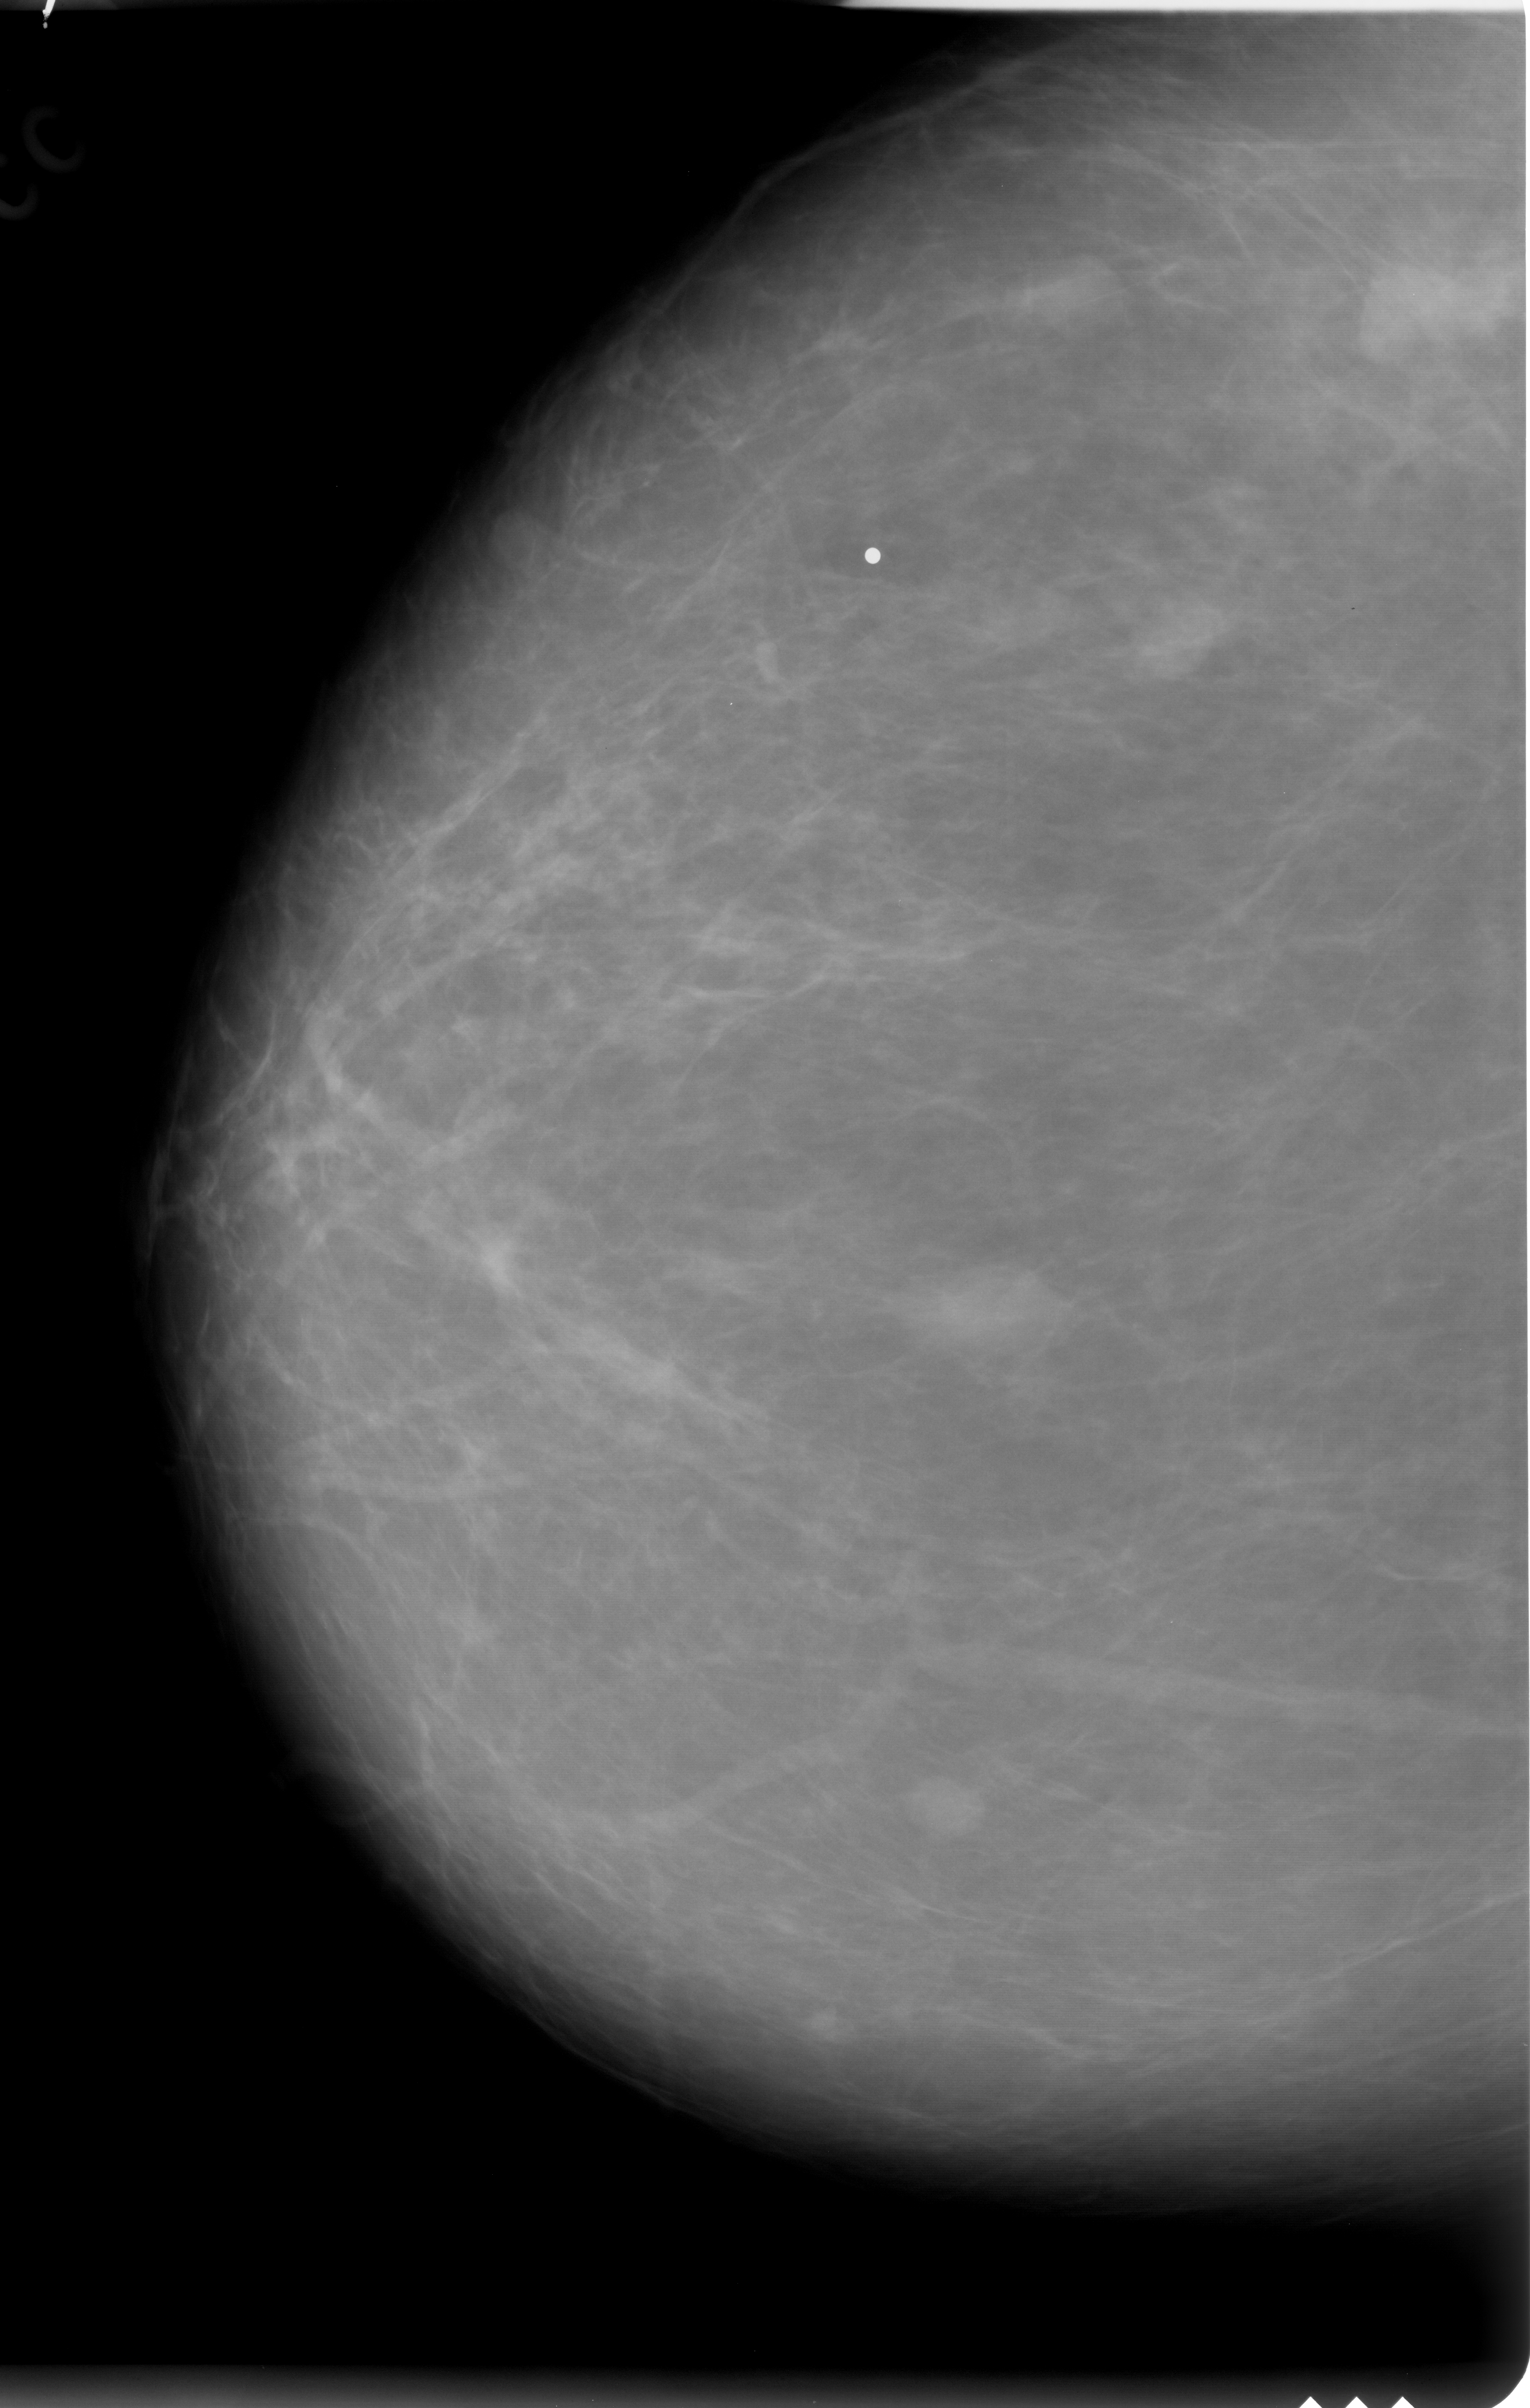
Scanned film-screen mammogram, right breast, CC view, breast composition: almost entirely fatty (BI-RADS density category 1 of 4).
- Marked findings (only marked abnormalities are described; nothing is implied about the rest of the image): Finding 1 of 5: mass, shape round, margins circumscribed; BI-RADS assessment category 2; pathology result (as recorded, not read from the image): benign.
- Finding 2 of 5: mass, shape round, margins circumscribed; BI-RADS assessment category 2; pathology (as recorded): benign.
- Finding 3 of 5: mass, shape round, margins circumscribed; BI-RADS assessment category 2; pathology (as recorded): benign.
- Finding 4 of 5: mass, shape round, margins circumscribed; BI-RADS assessment category 2; pathology result (as recorded, not read from the image): benign.
- Finding 5 of 5: mass, shape round, margins circumscribed; BI-RADS assessment category 2; pathology result (as recorded, not read from the image): benign.